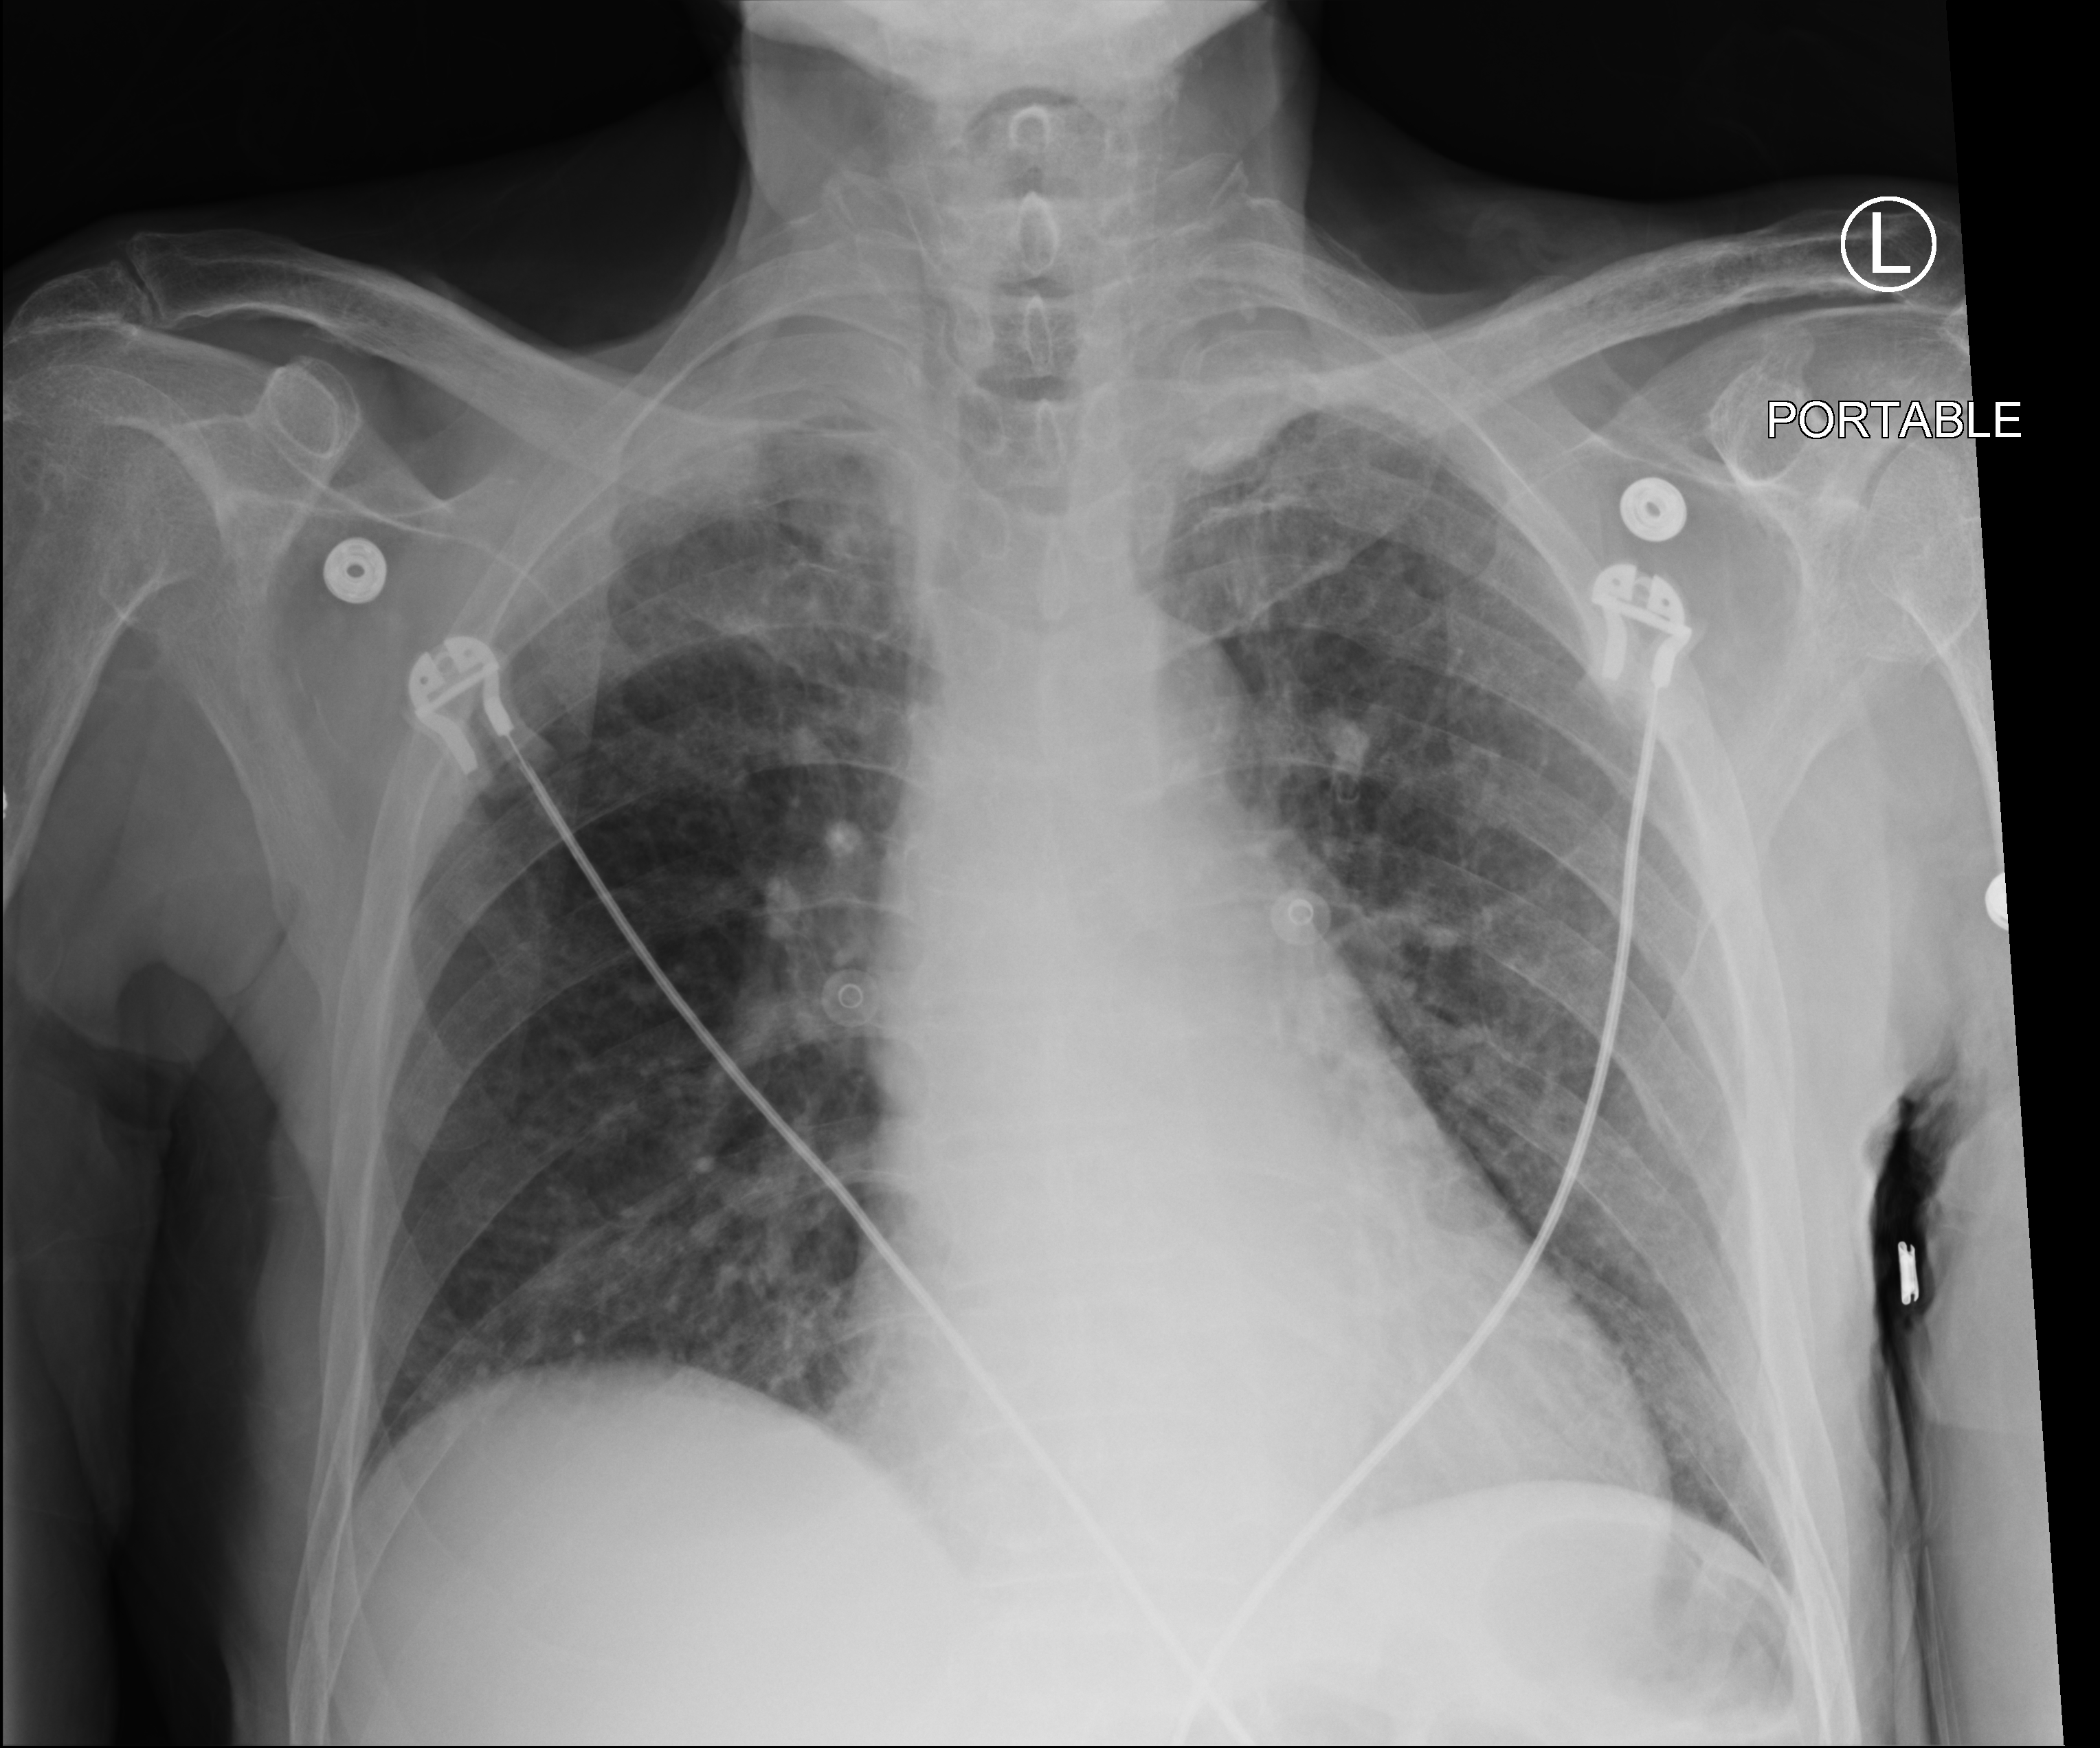
Chest X-ray (portable). Patient hospitalised with COVID-19; male, aged 75–90 years.
From the hospital-stay record, not from the radiograph (when in the stay this image was taken is not recorded): chronic kidney disease (admission record): no; admitted to intensive care during this hospital stay: no.